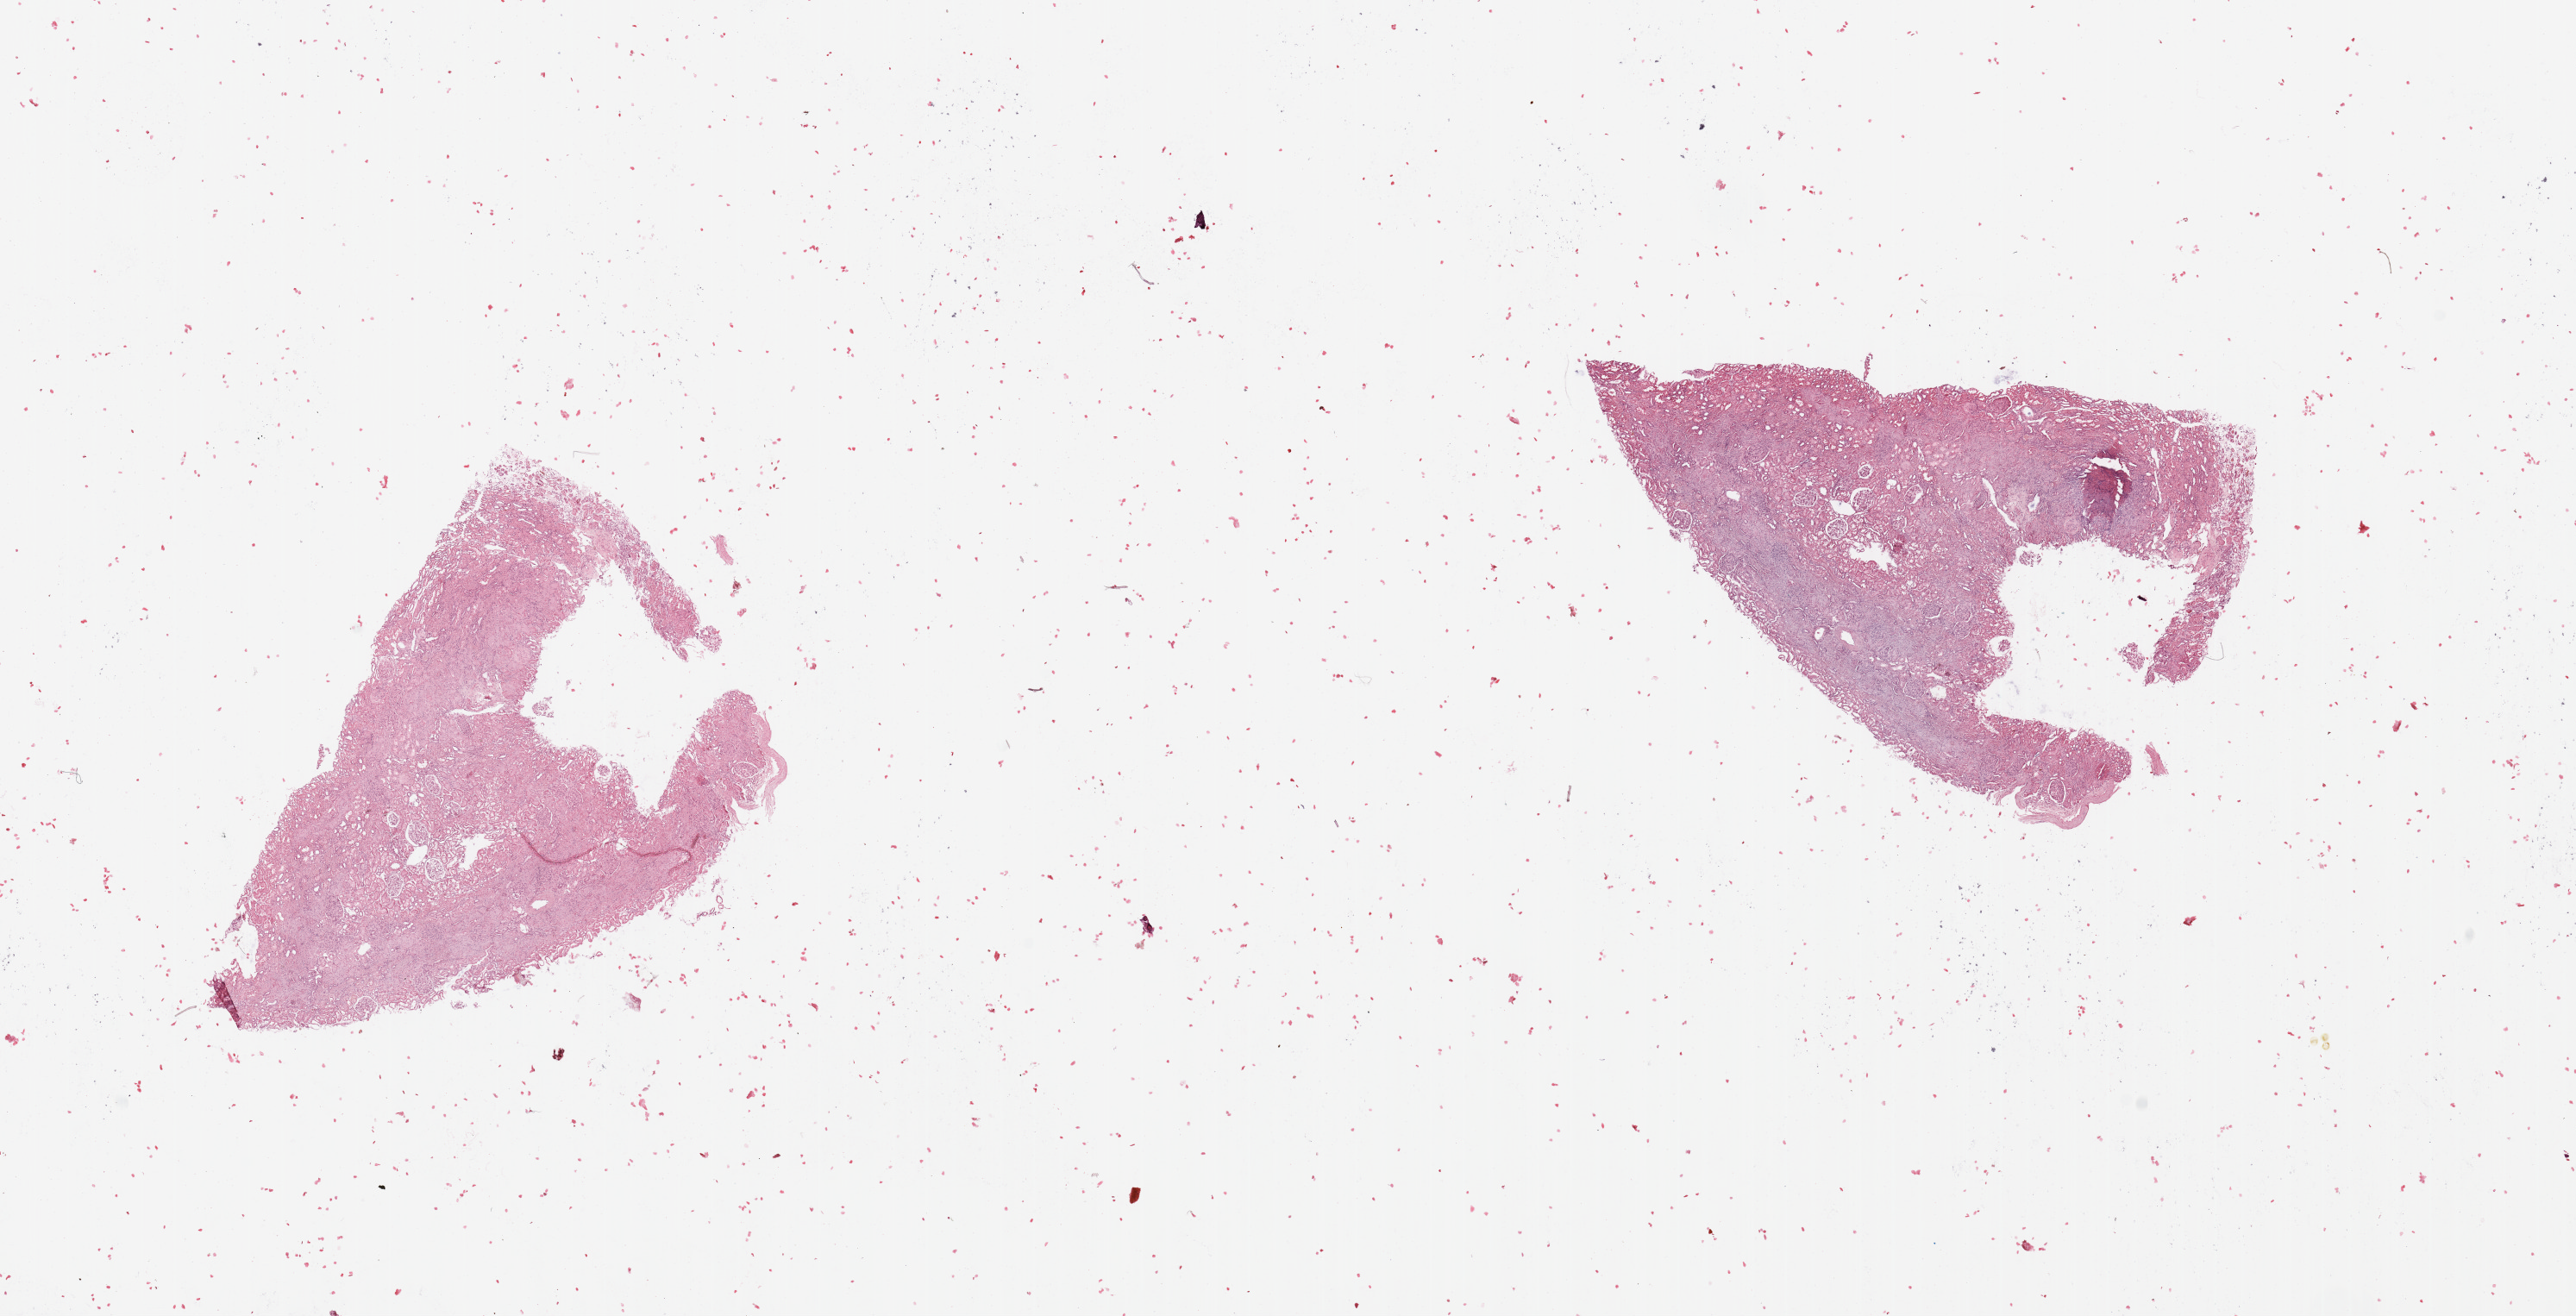
Whole-slide histology image, H&E-stained, low-resolution overview of the scanned area, about 23.6 x 12.1 mm, normal (non-tumour) tissue sample, sampled site: kidney. 50-year-old male patient.
- this section: normal (non-tumour) tissue from the same patient
- patient diagnosis: Renal cell carcinoma, NOS